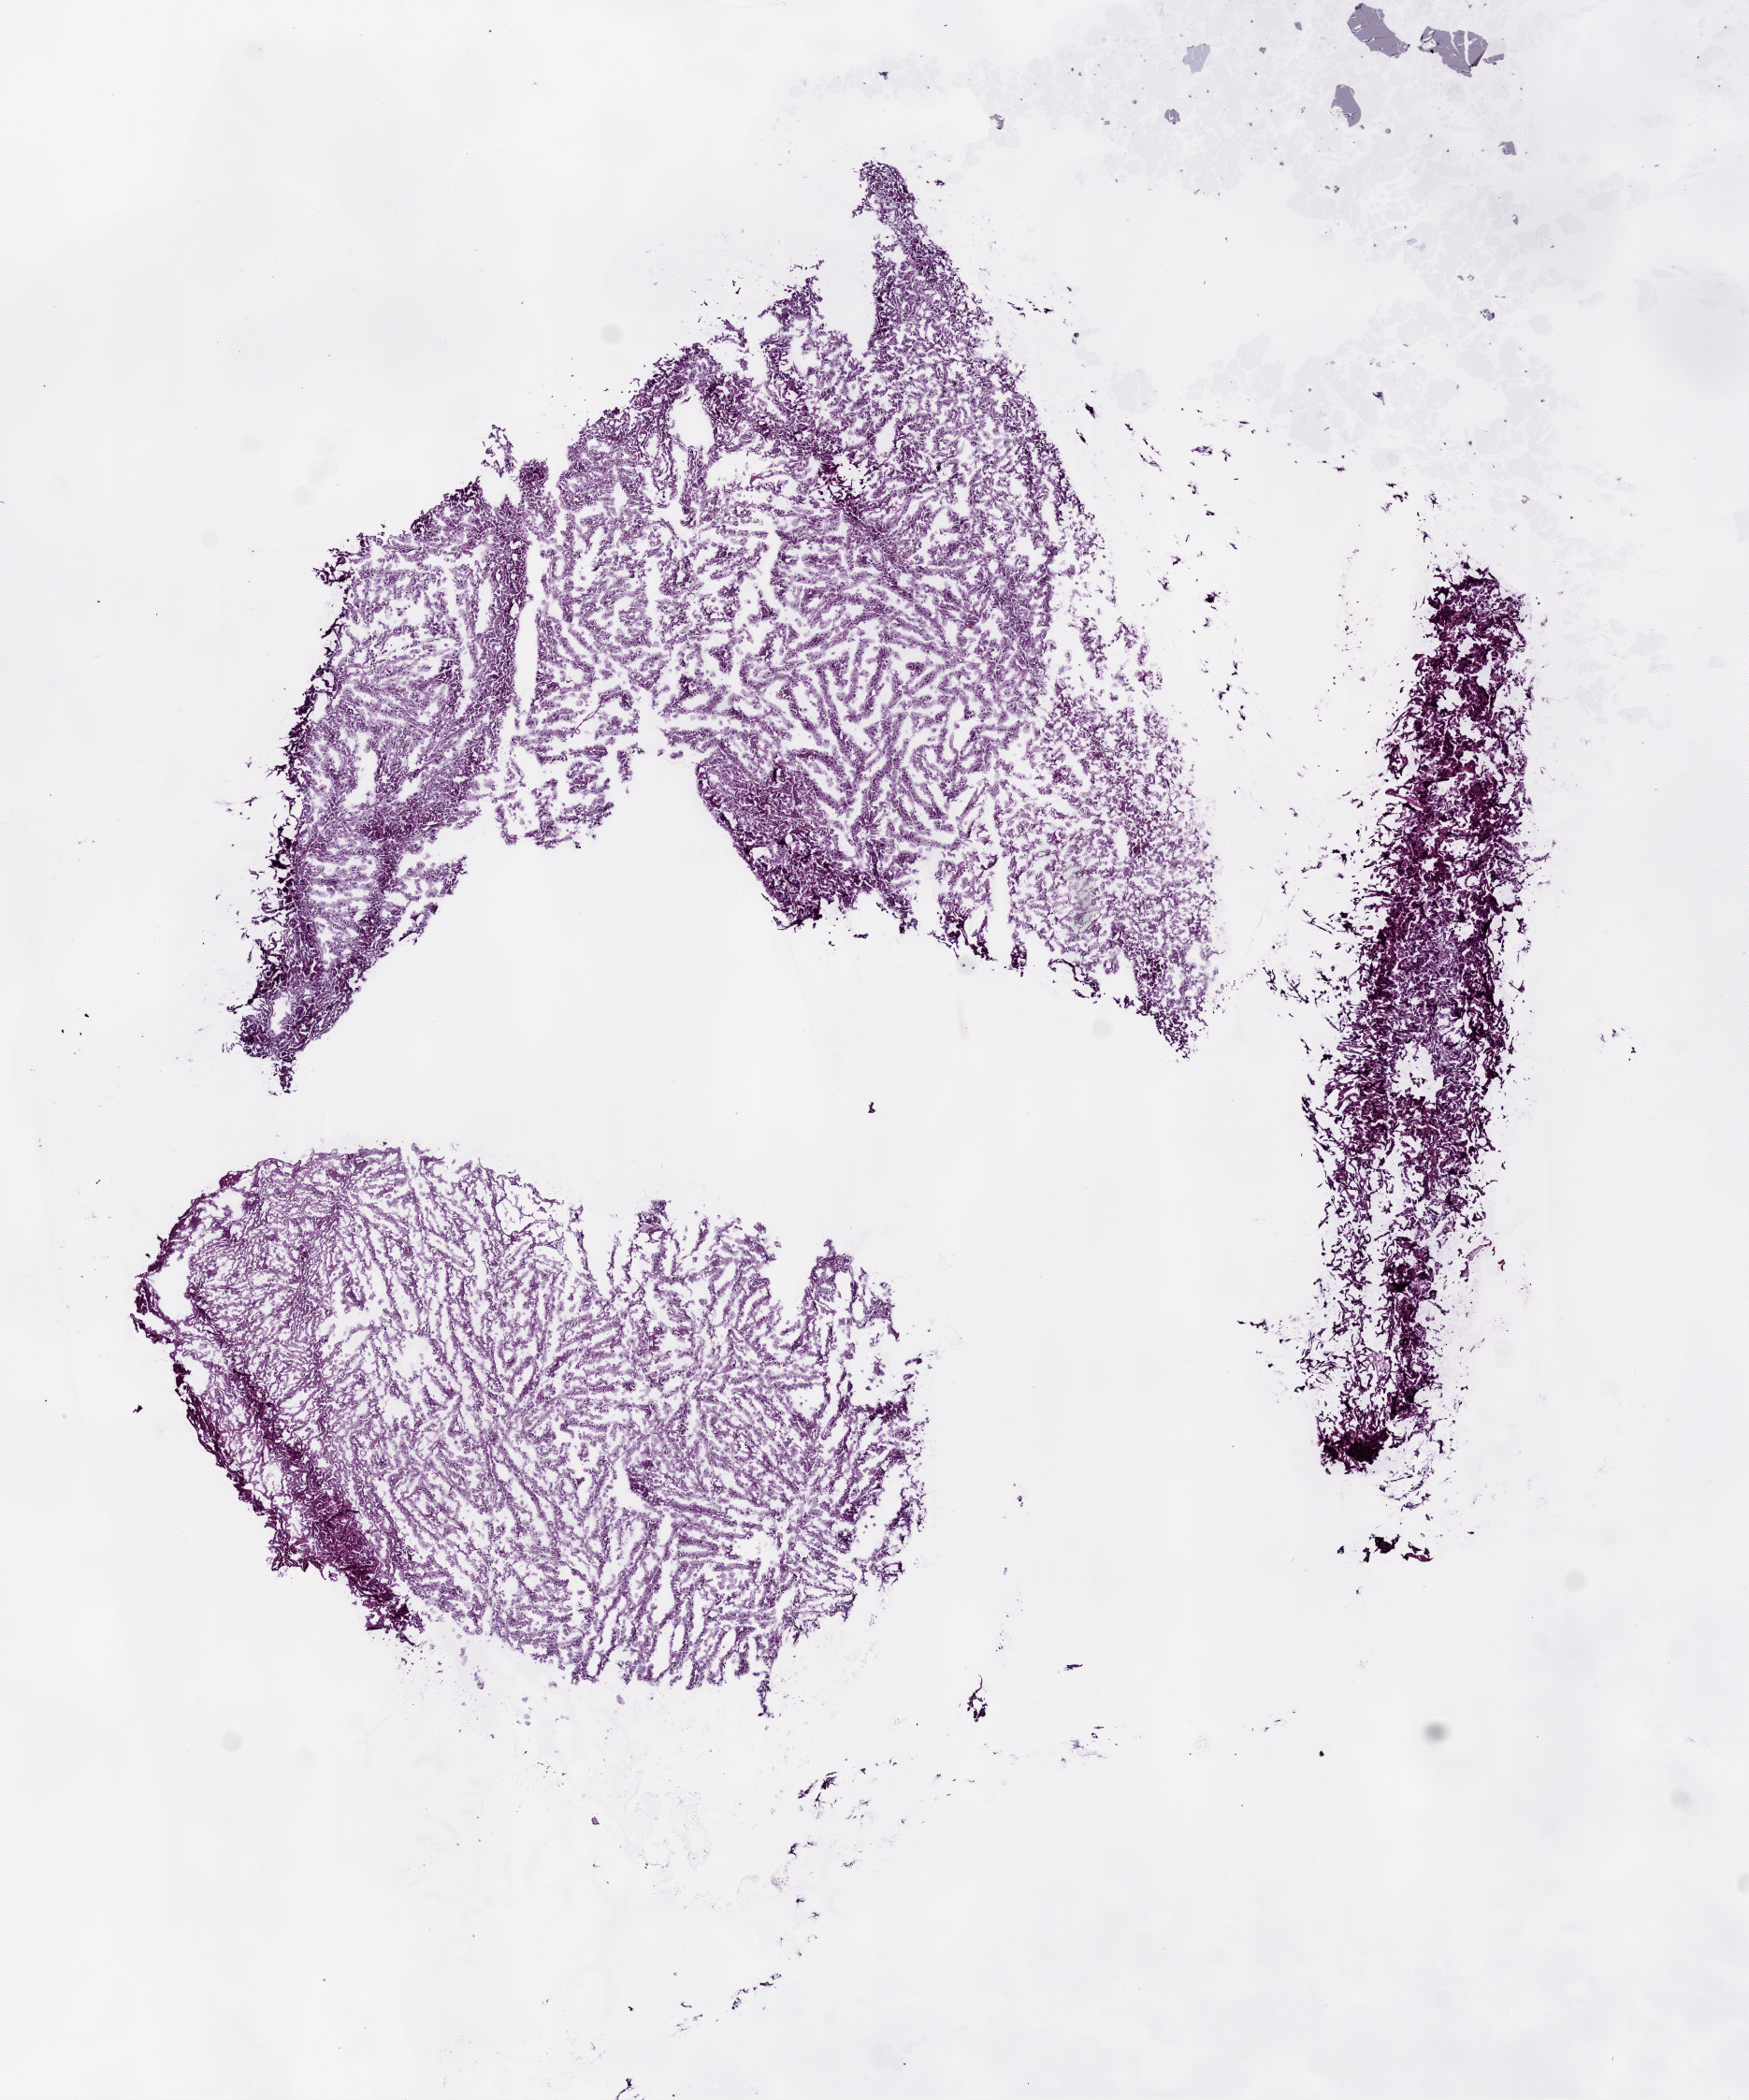
Whole-slide histology image, H&E, a low-resolution overview of the entire scanned area, about 7.5 x 9.0 mm (from a 5x scan); frozen section from the bottom of the tissue portion; brain, primary tumour sample. Male, age 40 years at initial diagnosis. Histologic grade: G3 (poorly differentiated). Composition of this section per pathologist review: tumour cells 100%, tumour nuclei 80%, normal cells 0%, stromal cells 0%, necrosis 0%.
• pathologic diagnosis: Astrocytoma, anaplastic
• laterality: left